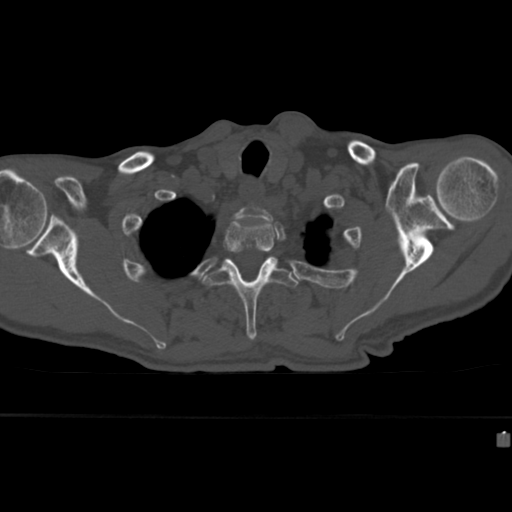
CT including the spine, one axial slice; slice 338 of 430 in the series (ordered by position); reconstruction kernel Br40s; bone window (W 1800 / L 400 HU); 1.5 mm slice thickness; 512 × 512 image matrix. Patient: male, 64 years. Case-level facts recorded for this patient, not image findings: primary cancer: uterus.
Structures marked on this image (semi-automatic segmentation, software-assisted and operator-edited):
- T2 vertebra: box from (x=215, y=218) to (x=276, y=263) px
- T3 vertebra: (x=202, y=257)–(x=299, y=341)